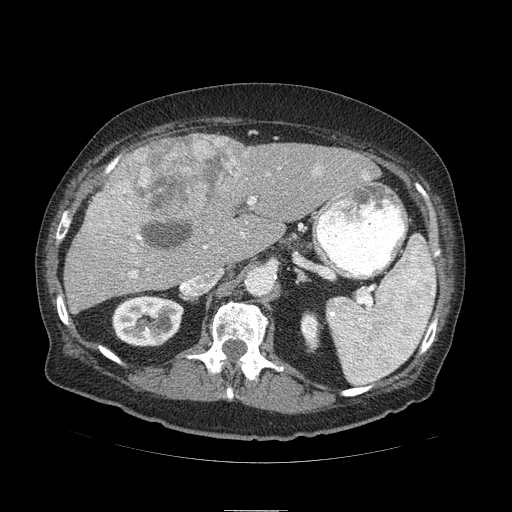
Contrast-enhanced abdominal CT (liver protocol), one axial slice; position 56 of 103 along the scan axis; soft-tissue window (W 400 / L 40 HU); 2.5 mm slice thickness; 512 × 512 image matrix, field of view 440 × 440 mm. From the clinical record (not read from this slice): diagnosis: hepatocellular carcinoma (patient treated with transarterial chemoembolisation; whether this scan precedes or follows treatment is not stated here); TNM stage (as recorded): Stage-IIIA; Child-Pugh class: B; tumour size: 13 cm.
Structures marked on this image (semi-automatically segmented with operator editing):
- liver parenchyma outside the tumour (the mass and vessels are separate outlines, so this box may not span the whole liver): box from (x=64, y=134) to (x=378, y=312) px
- mass: (x=82, y=132)–(x=246, y=249)
- liver vessels: (x=130, y=176)–(x=369, y=278)